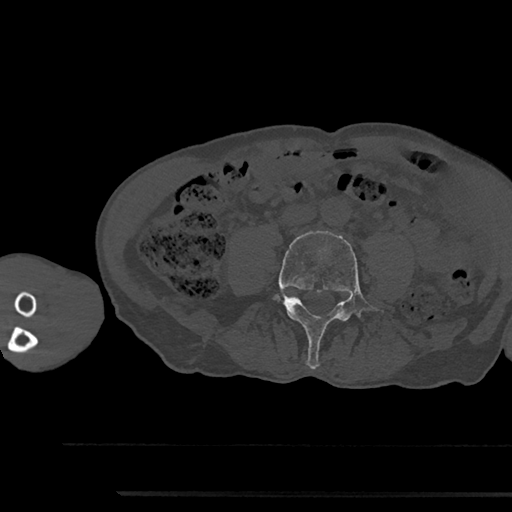
CT including the spine, one axial slice. Slice 411 of 797 in the series (ordered by position). 120 kVp. Bone window (W 1800 / L 400 HU). 0.5 mm slice thickness. 512 × 512 image matrix, field of view 367 × 367 mm. Male patient, age 79 years. From the clinical record (not read from this slice): primary cancer: prostate.
Annotated regions visible in this slice (semi-automatically segmented with operator editing):
- L4 vertebra: box from (x=275, y=231) to (x=384, y=369) px